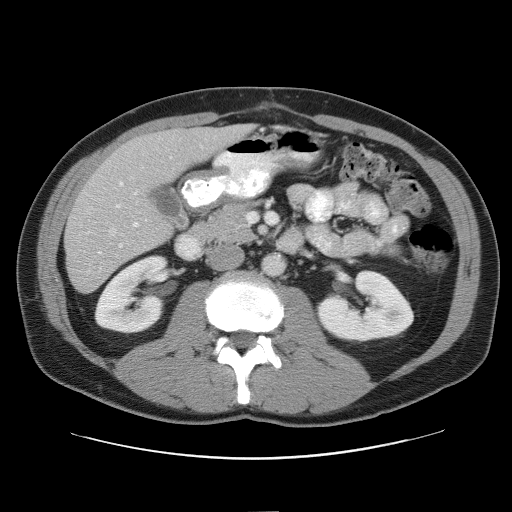
Contrast-enhanced abdominal CT, one axial slice; position 25 of 52 along the scan axis; reconstruction kernel STANDARD; 120 kVp; intravenous contrast given; soft-tissue window (W 400 / L 40 HU); 5 mm slice thickness; 512 × 512 image matrix, field of view 393 × 393 mm. Male patient, age 70 years. Case-level facts recorded for this patient, not image findings: diagnosis: colorectal cancer liver metastases, imaged before liver resection; multiple liver metastases: yes; largest metastasis: 4 cm; chemotherapy before resection: yes.
Outlined on this slice (expert manual segmentation):
- hepatic veins: bounding box [x1, y1, x2, y2] px = [85, 176, 135, 255]
- liver: [66, 126, 246, 293]
- planned liver remnant (the part of the liver to remain after resection): [119, 126, 247, 186]
- portal vein (with intrahepatic branches): [115, 181, 139, 227]